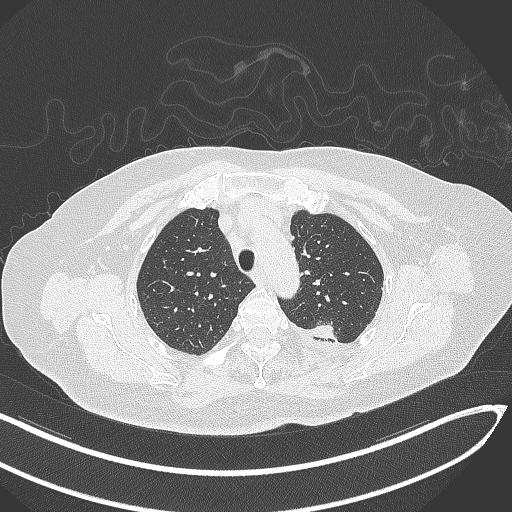
Chest CT, one axial slice. Slice 251 of 270 in the series (ordered by position). 120 kVp. Lung window (W 1500 / L -600 HU). 1 mm slice thickness. 512 × 512 image matrix. Female patient, age 76 years. Case-level facts recorded for this patient, not image findings: clinical TNM (as recorded): T1c N0 M0.
Outlined on this slice (rectangle marked by the reading radiologist):
- lung tumour (recorded histology: adenocarcinoma): bounding box <305,321,339,344> (left, top, right, bottom; pixels)